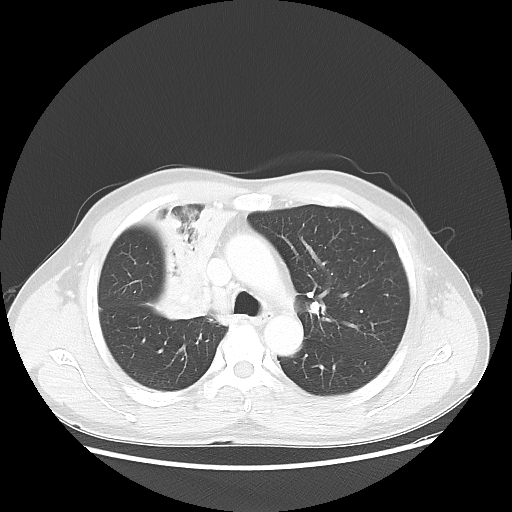
Chest CT, one axial slice. Position 37 of 56 along the scan axis. Reconstruction kernel LUNG. 100 kVp. Lung window (W 1500 / L -600 HU). 5 mm slice thickness. 512 × 512 image matrix, field of view 398 × 398 mm. Male patient, age 60 years. Case-level facts recorded for this patient, not image findings: clinical TNM (as recorded): T2a N1 M0.
Annotated regions visible in this slice (bounding box drawn by a radiologist):
- lung tumour (recorded histology: squamous cell carcinoma): box from (x=133, y=194) to (x=236, y=323) px